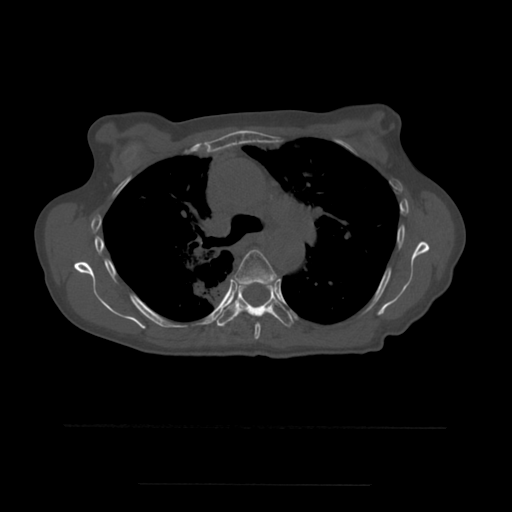
CT including the spine, one axial slice. Bone window (W 1800 / L 400 HU). 512 × 512 image matrix, field of view 350 × 350 mm. Patient age 58 years. Case-level facts recorded for this patient, not image findings: primary cancer: lung.
Structures marked on this image (semi-automatically segmented with operator editing):
- T5 vertebra: bounding box (x1, y1, x2, y2) in pixels: (234, 250, 278, 340)
- T6 vertebra: (216, 283, 294, 327)